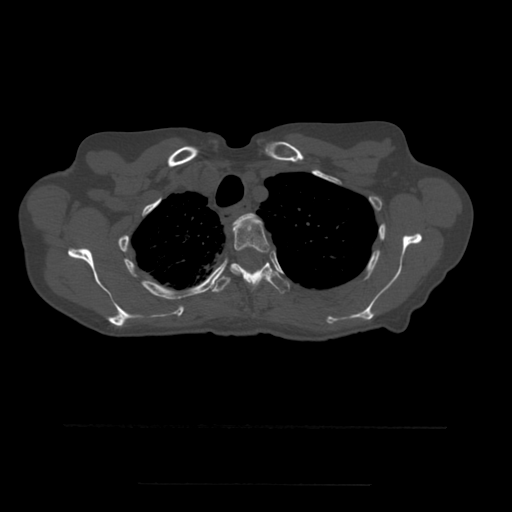
CT including the spine, one axial slice. Position 416 of 544 along the scan axis. Bone window (W 1800 / L 400 HU). 1.25 mm slice thickness. 512 × 512 image matrix. Patient age 58 years. From the clinical record (not read from this slice): primary cancer: lung.
Annotated regions visible in this slice (semi-automatic segmentation, software-assisted and operator-edited):
- T2 vertebra: bounding box <233,213,259,229> (left, top, right, bottom; pixels)
- T3 vertebra: <231,219,271,282>
- T4 vertebra: <211,262,290,293>